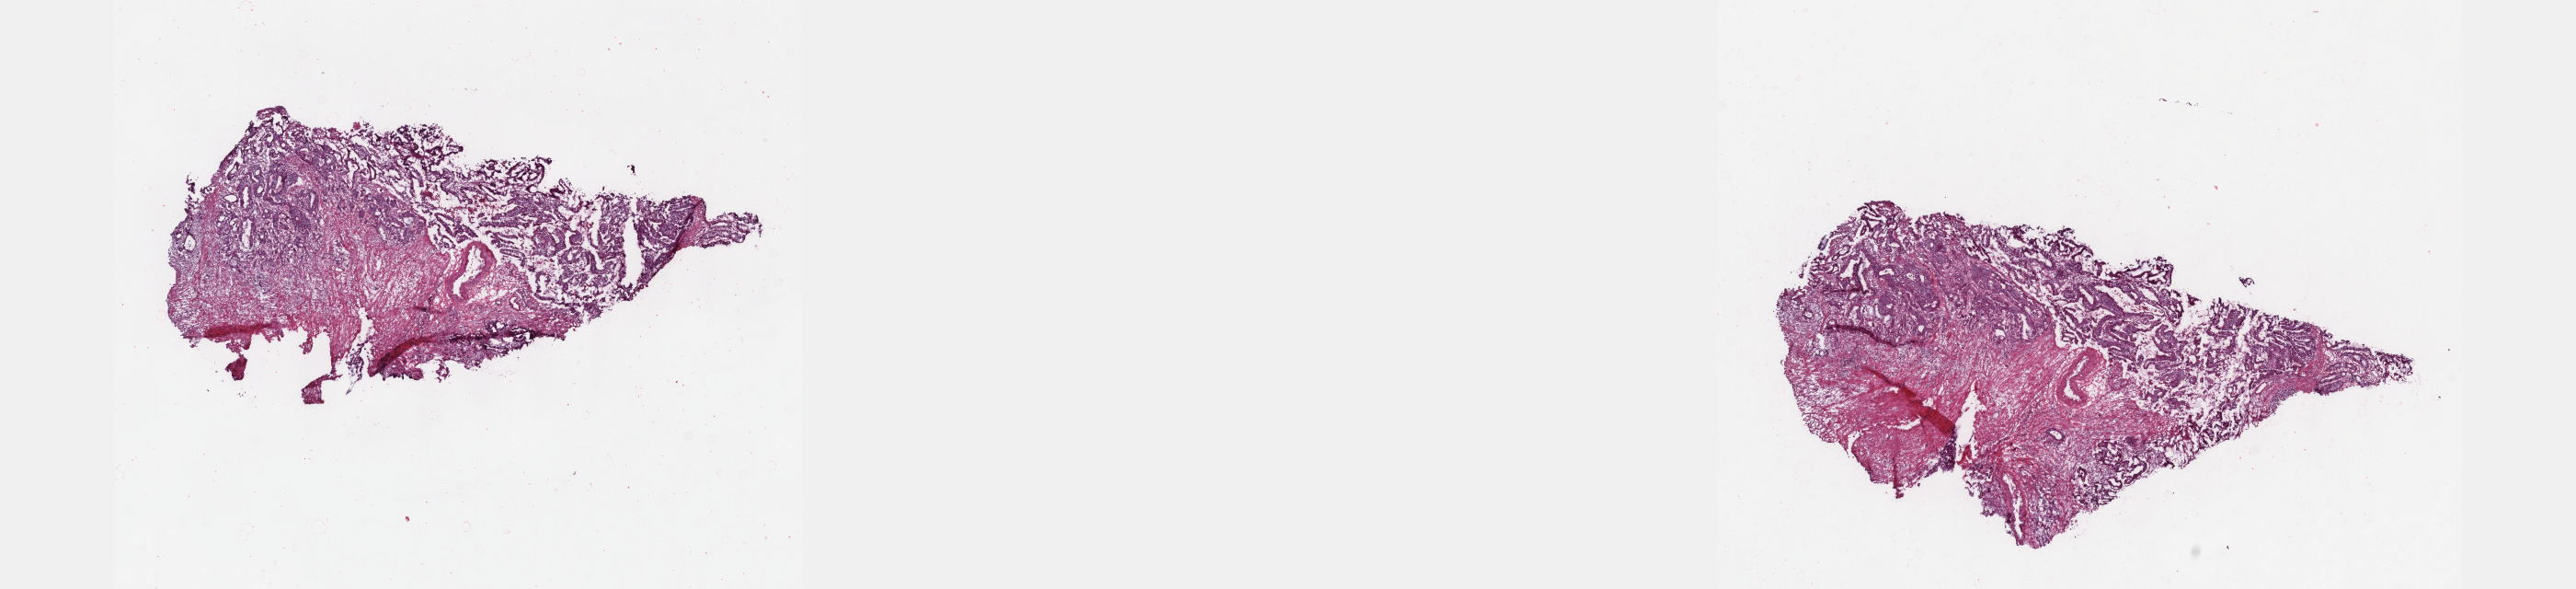
H&E-stained whole-slide image, whole scanned area (about 22.6 x 5.2 mm) shown as a low-resolution overview, frozen section from the bottom of the tissue portion, primary tumour sample from the rectum. Patient: male, age at initial diagnosis 68 years. Pathologist review of this section (percent, as recorded): tumour cells 63%, tumour nuclei 75%, normal cells 0%, stromal cells 35%, necrosis 2%. Infiltration values recorded for this section: lymphocyte infiltration 14%, monocyte infiltration 4%, neutrophil infiltration 2%.
AJCC pathologic stage: IIIB (6th edition). Histologic diagnosis: Adenocarcinoma, NOS. Lymph nodes positive (case pathology): 2 of 16 examined. TNM: T3 N1 M0.